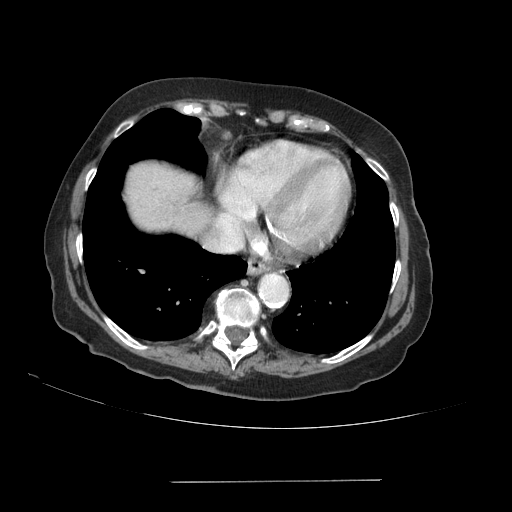
Contrast-enhanced abdominal CT (liver protocol), one axial slice; position 82 of 89 along the scan axis; 140 kVp; soft-tissue window (W 400 / L 40 HU); 2.5 mm slice thickness; 512 × 512 image matrix, field of view 400 × 400 mm. From the clinical record (not read from this slice): diagnosis: hepatocellular carcinoma (patient treated with transarterial chemoembolisation; whether this scan precedes or follows treatment is not stated here); TNM stage (as recorded): Stage-IVA; Child-Pugh class: A; tumour nodularity: uninodular.
Structures marked on this image (semi-automatically segmented with operator editing):
- liver parenchyma outside the tumour (the mass and vessels are separate outlines, so this box may not span the whole liver): bounding box (x1, y1, x2, y2) in pixels: (126, 162, 208, 234)